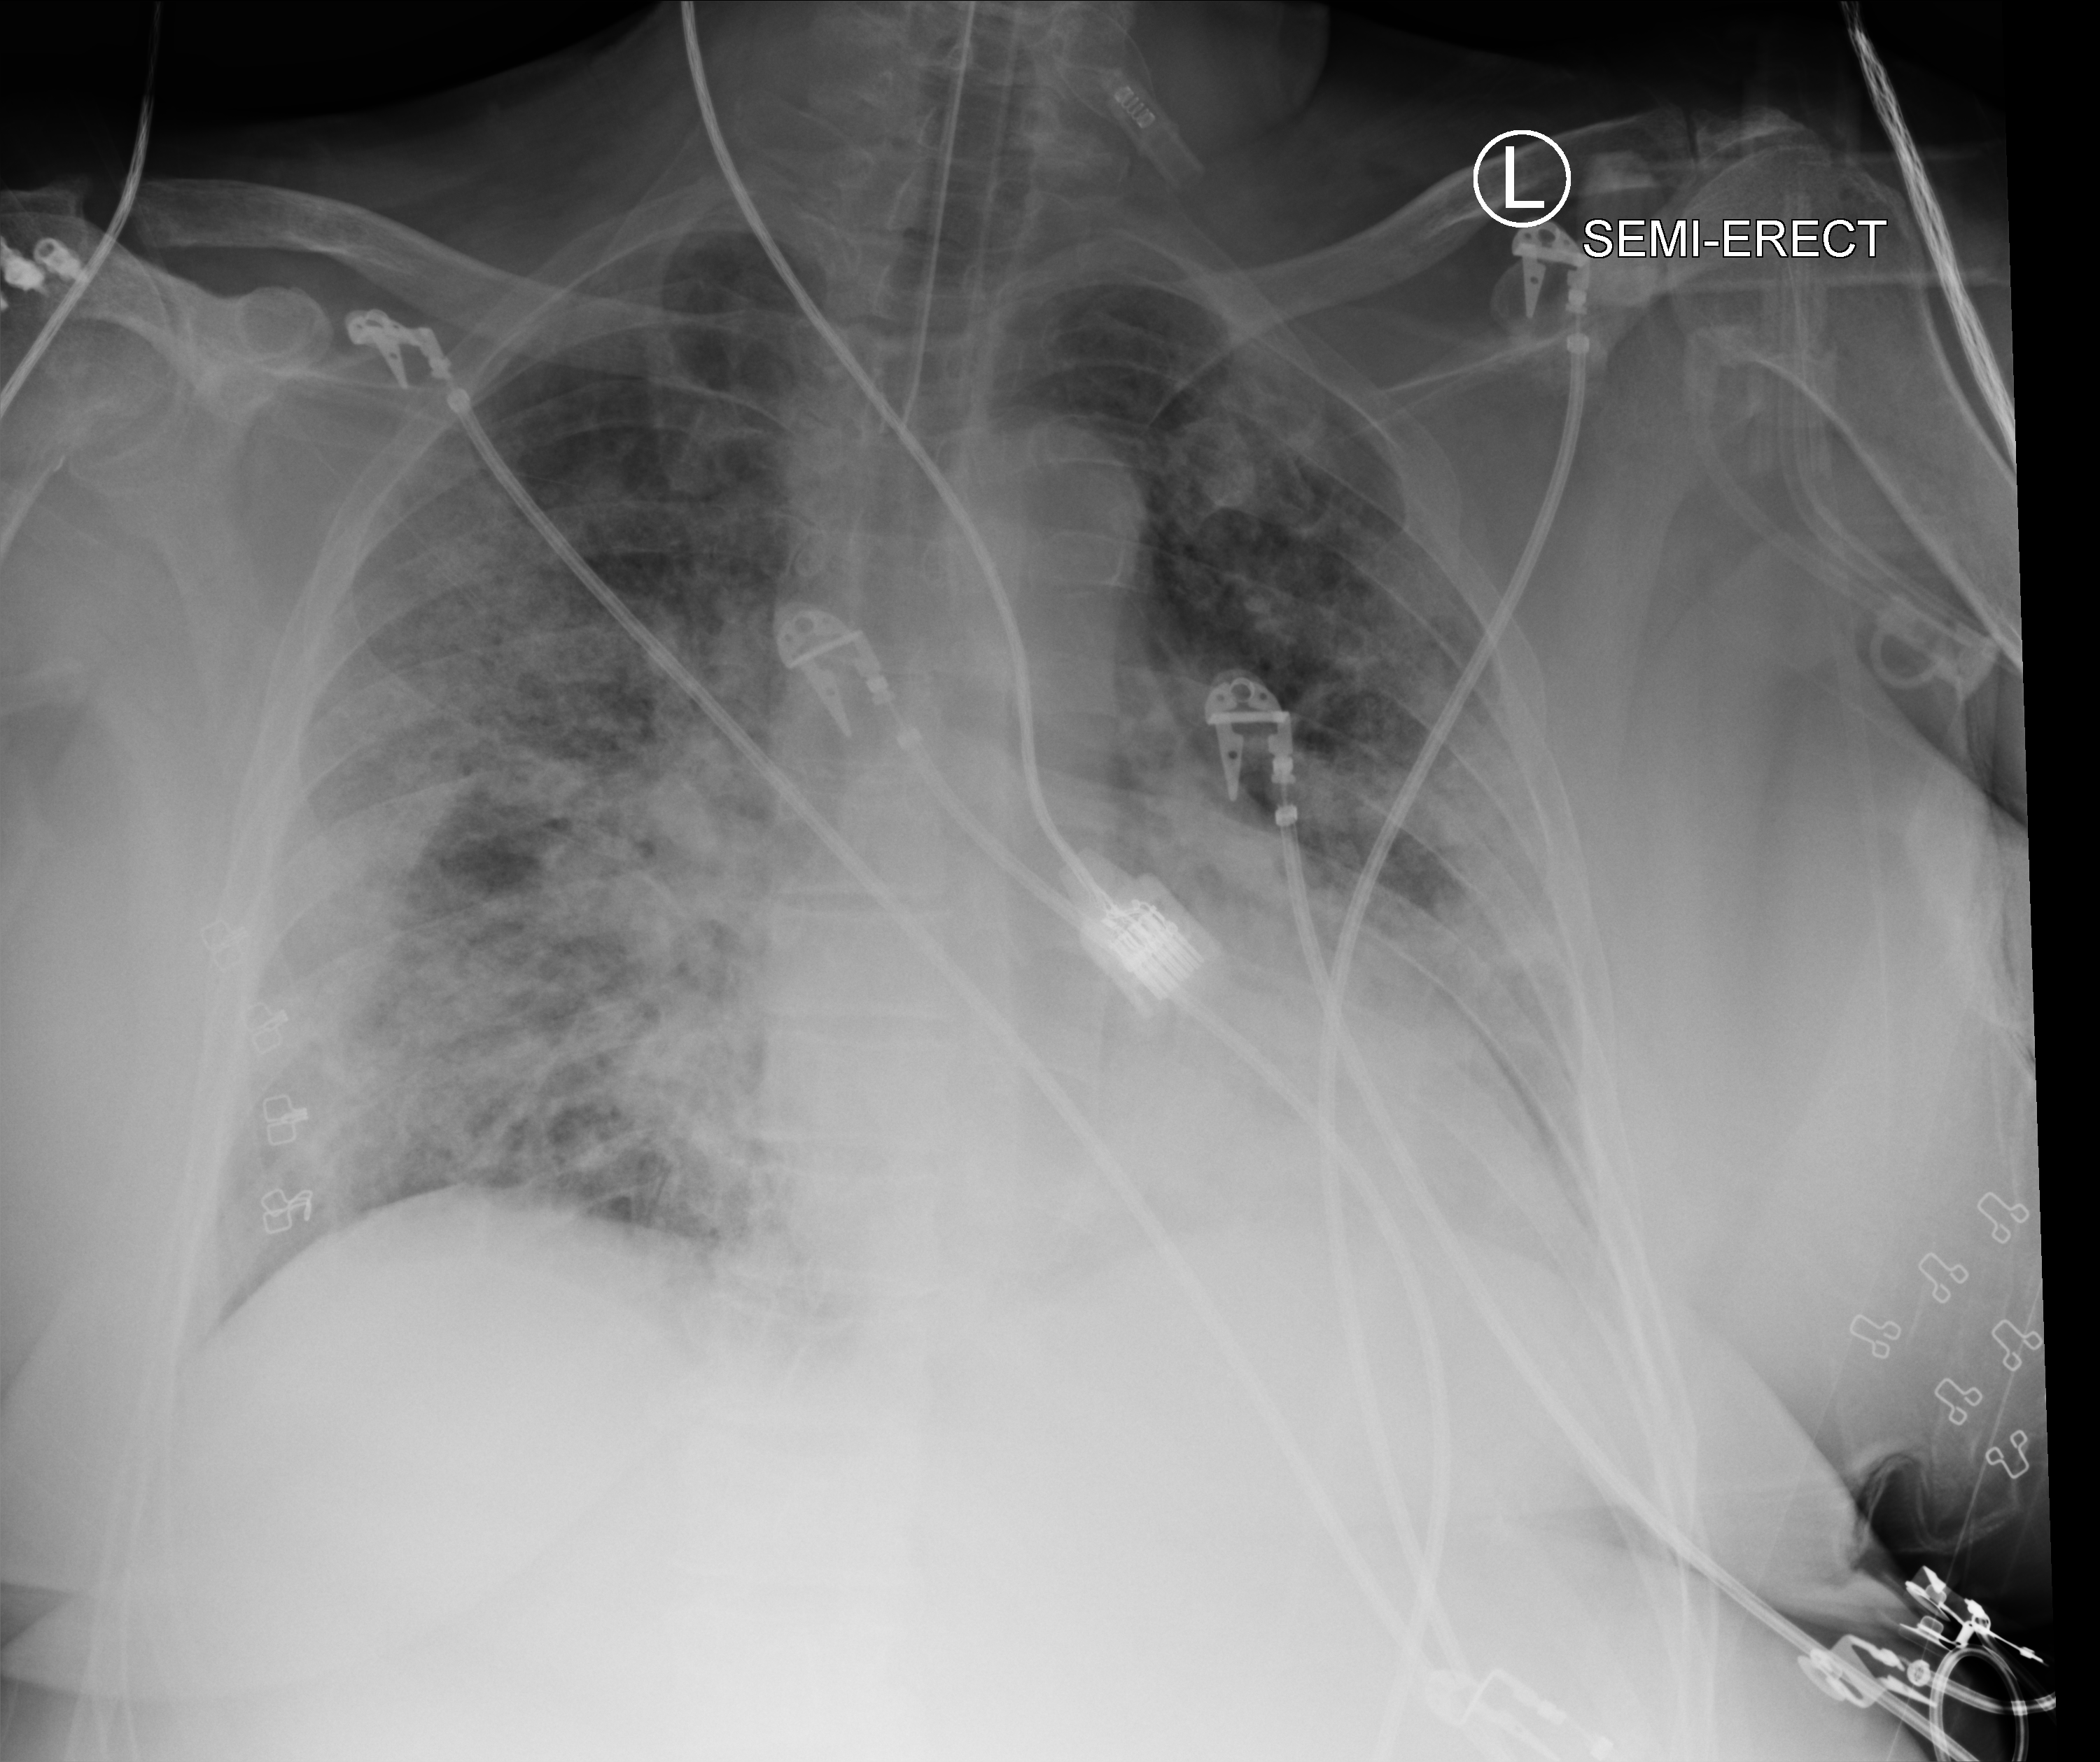
Chest X-ray (portable). Female patient hospitalised with COVID-19, age 60–74 years.
From the hospital-stay record, not from the radiograph (when in the stay this image was taken is not recorded): other chronic lung disease (admission record): no; mechanically ventilated during this hospital stay: yes.